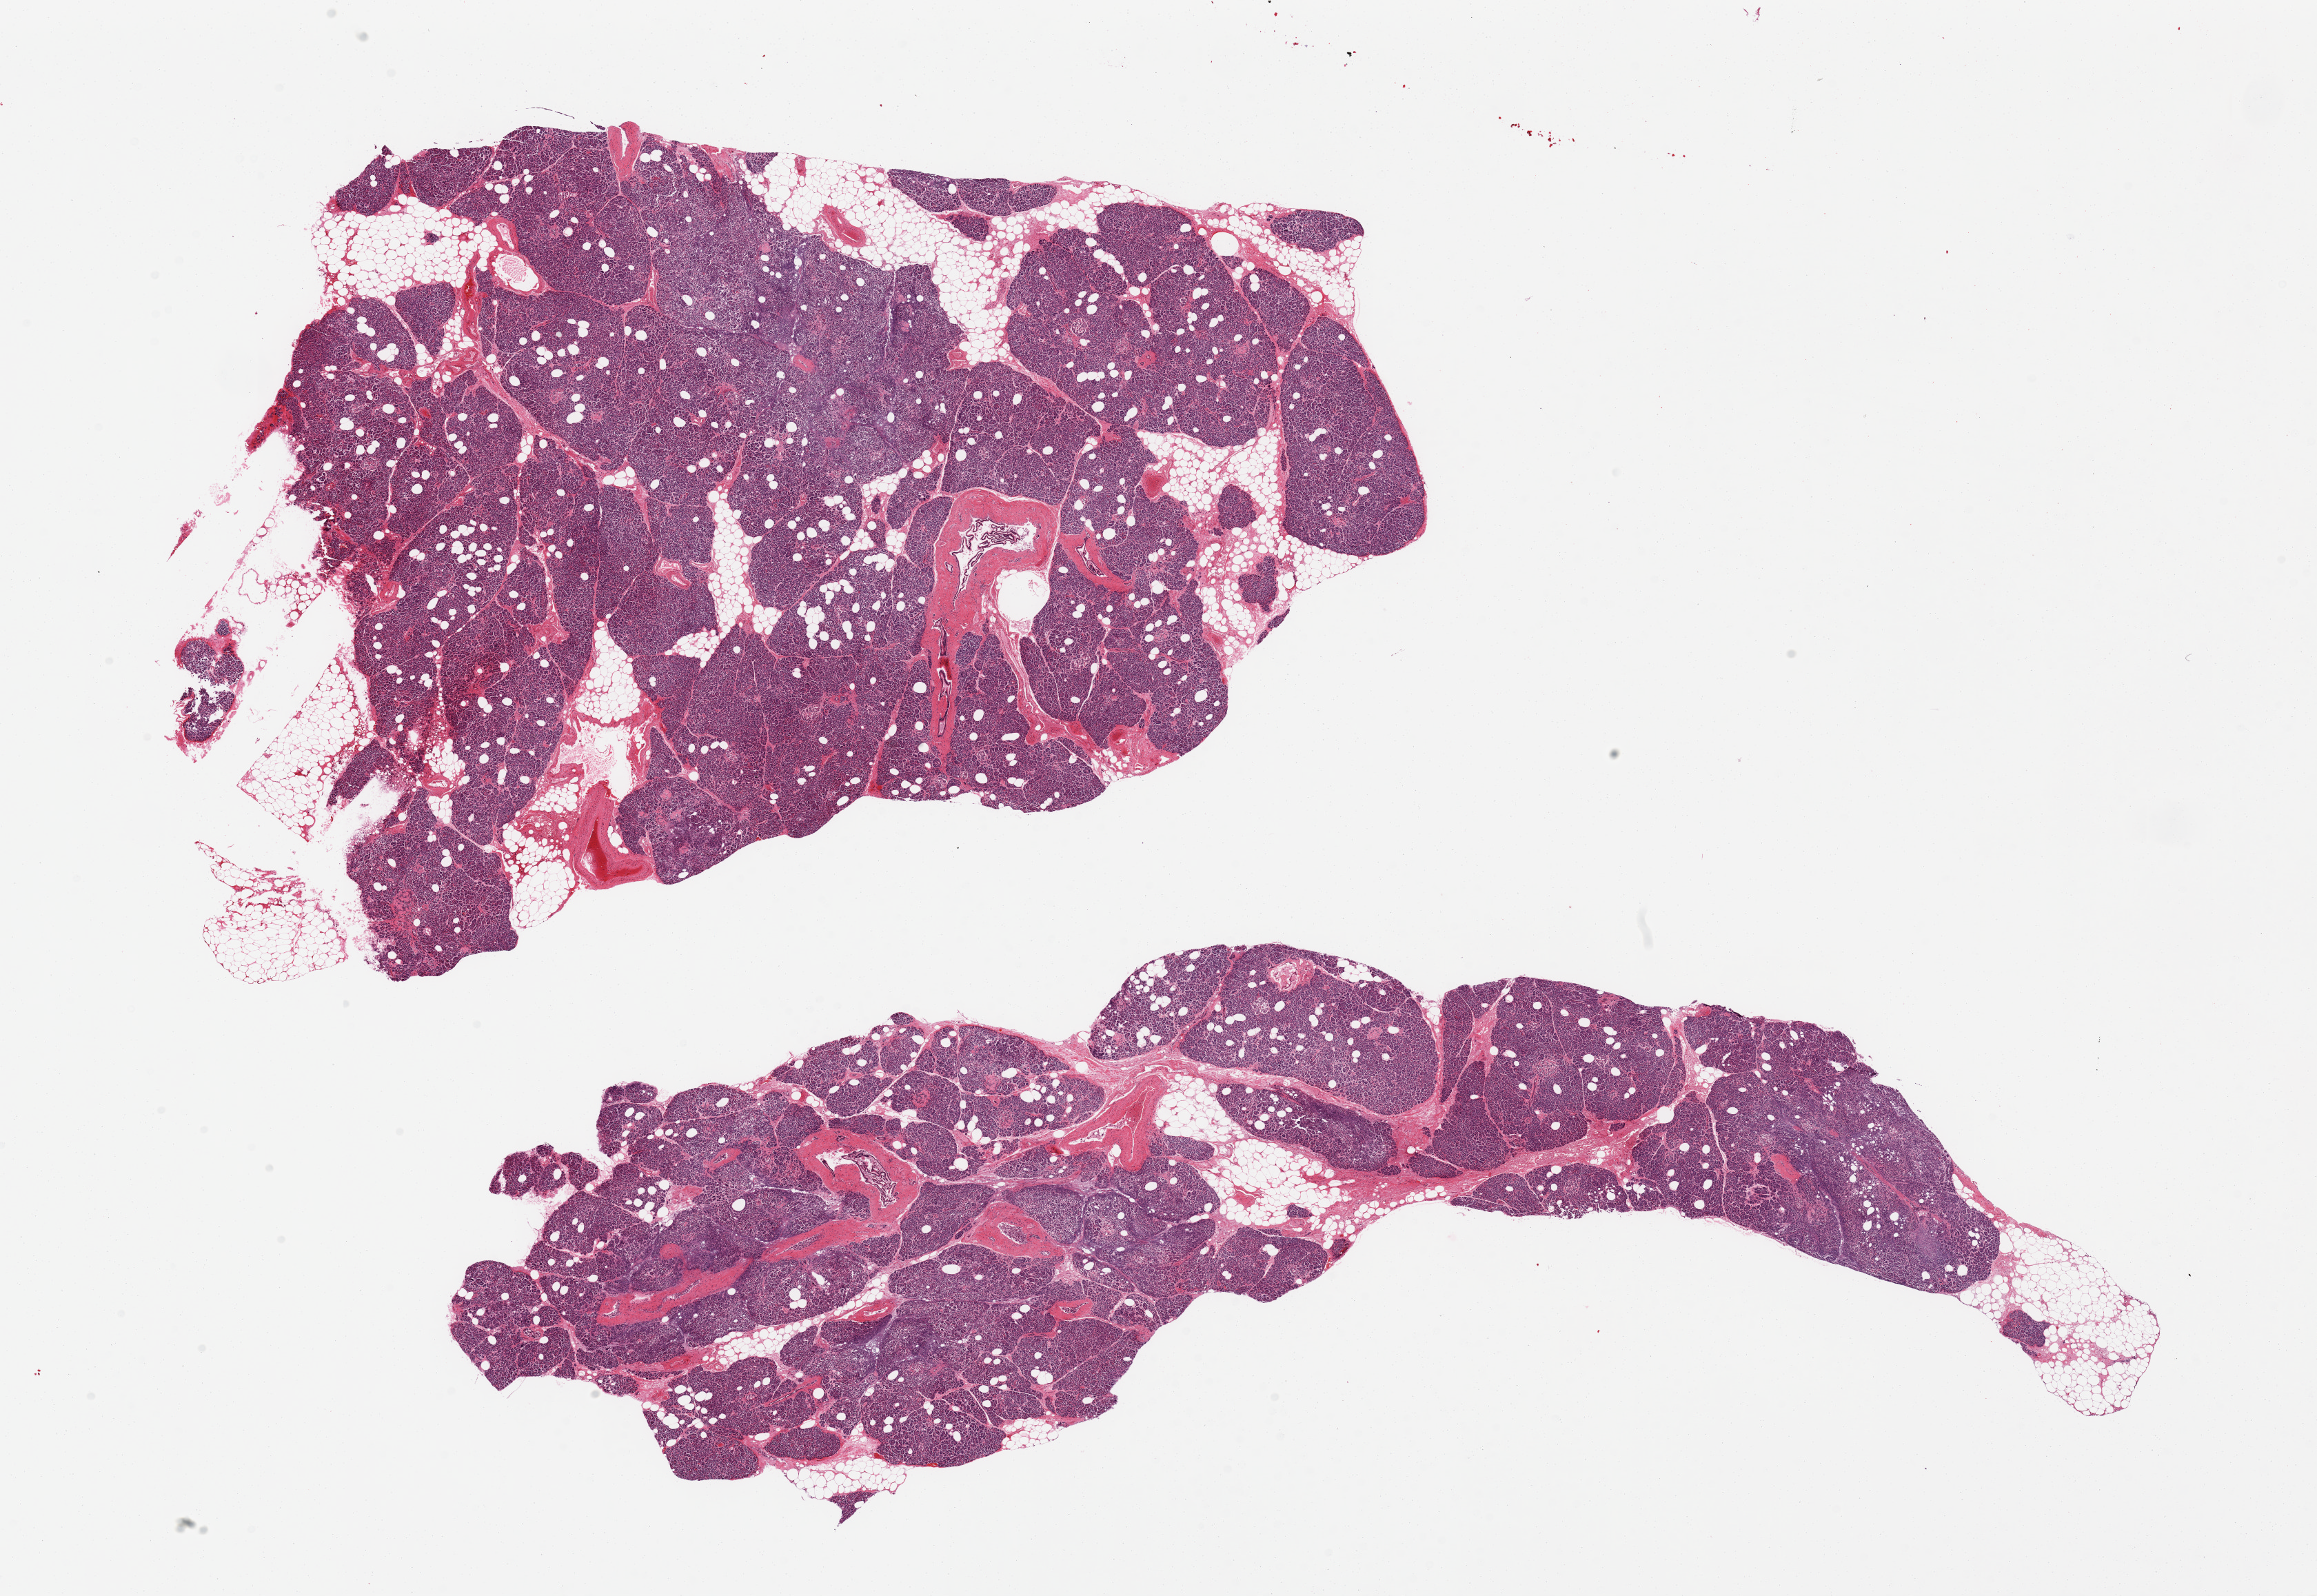
Haematoxylin and eosin whole-slide image — whole scanned area (about 26.6 x 18.3 mm, slide scanned at 20x) shown as a low-resolution overview, PAXgene-fixed paraffin-embedded (PFPE) section, section of pancreas (target tissue), donor tissue sample. Female donor.
Reviewer comment on this tissue sample: 2 pieces, ~10% fat, islets reduced in number and some with amyloid-like material.